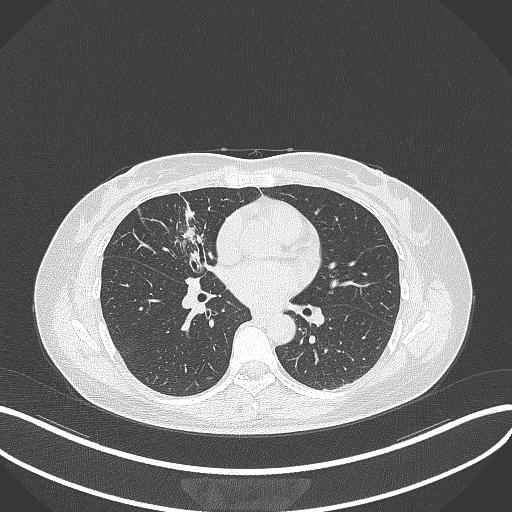
Chest CT, one axial slice; reconstruction kernel B70f; 120 kVp; lung window (W 1500 / L -600 HU); 1 mm slice thickness; 512 × 512 image matrix, field of view 400 × 400 mm. Patient: female, 43 years. From the clinical record (not read from this slice): clinical TNM (as recorded): T1c N3 M1.
Annotated regions visible in this slice (bounding box drawn by a radiologist):
- lung tumour (recorded histology: adenocarcinoma): bounding box (x1, y1, x2, y2) in pixels: (179, 220, 203, 246)